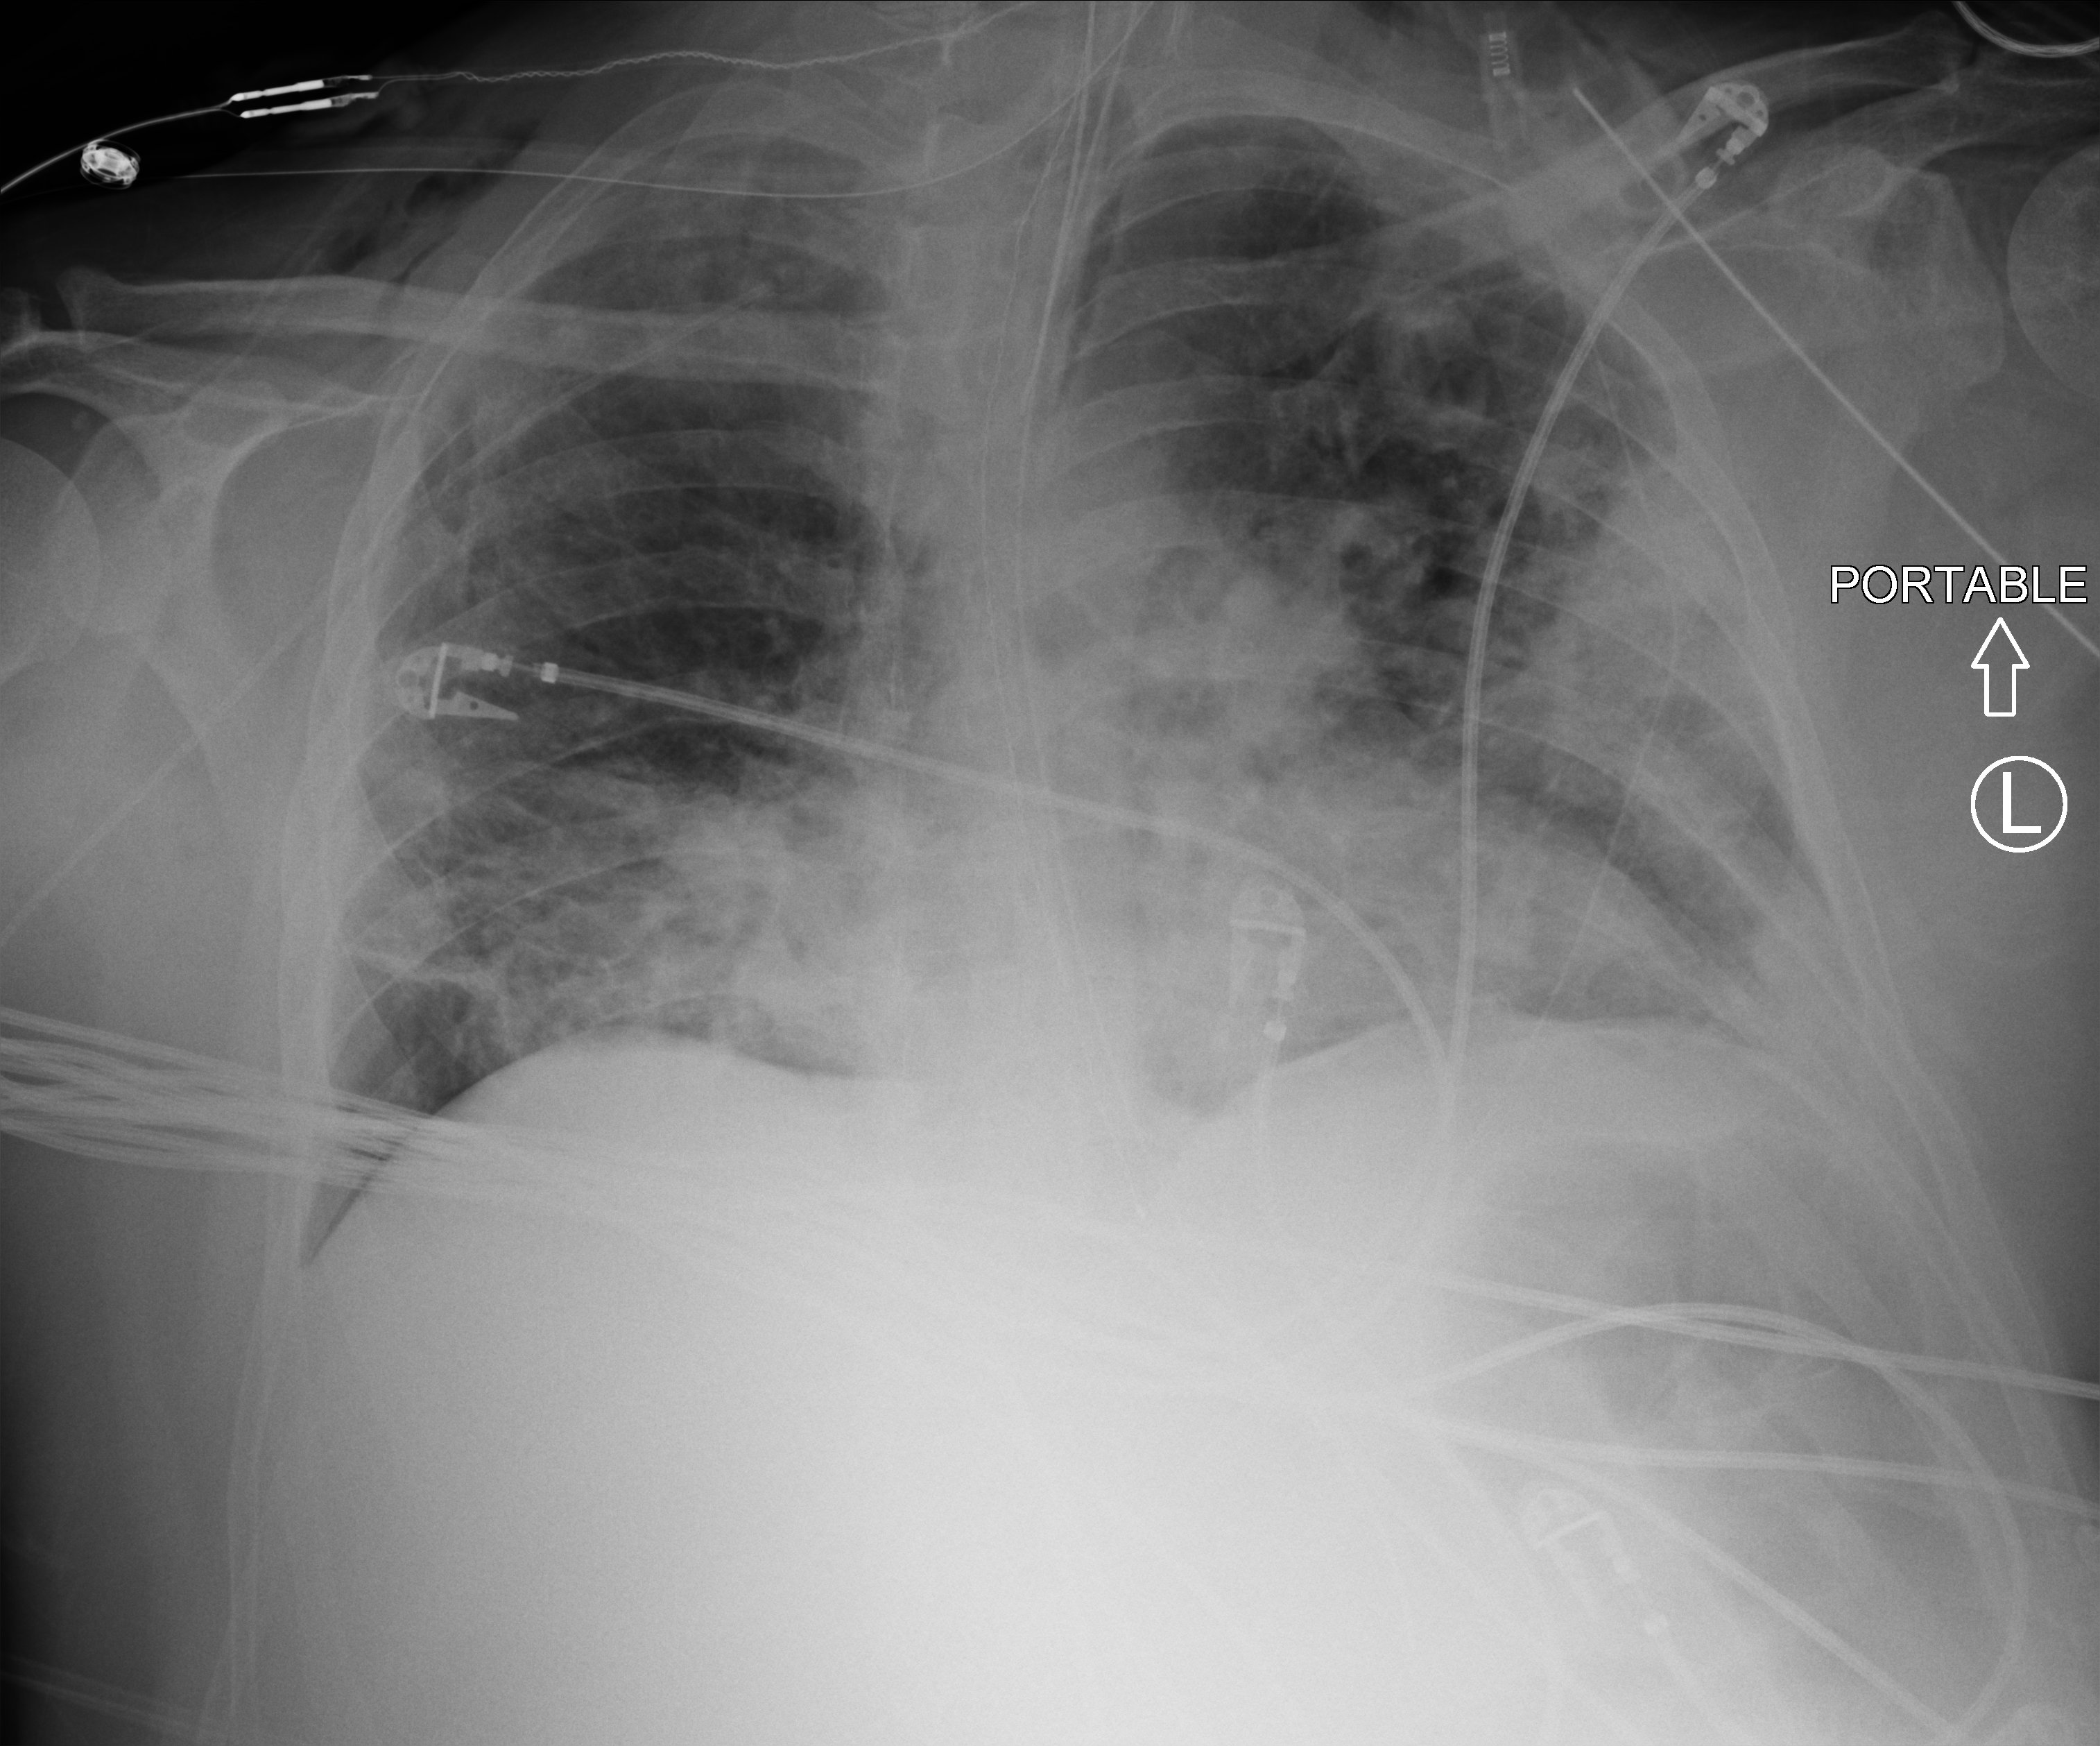
Chest X-ray (portable). Adult patient hospitalised with COVID-19, age 18–59 years.
Admission-level facts for this patient (not findings on this image; timing relative to this image not recorded):
- diabetes (admission record): no
- admitted to intensive care during this hospital stay: yes